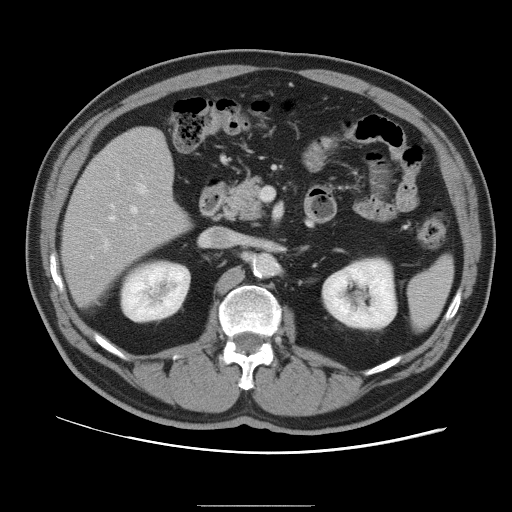
Contrast-enhanced abdominal CT, one axial slice; position 48 of 105 along the scan axis; 120 kVp; intravenous contrast given; soft-tissue window (W 400 / L 40 HU); 512 × 512 image matrix, field of view 399 × 399 mm. Male patient, age 64 years. From the clinical record (not read from this slice): diagnosis: colorectal cancer liver metastases, imaged before liver resection; multiple liver metastases: yes.
Structures marked on this image (expert manual segmentation):
- hepatic veins: bounding box [x1, y1, x2, y2] px = [91, 205, 149, 259]
- liver: [63, 129, 189, 306]
- planned liver remnant (the part of the liver to remain after resection): [64, 129, 189, 306]
- portal vein (with intrahepatic branches): [104, 183, 148, 249]